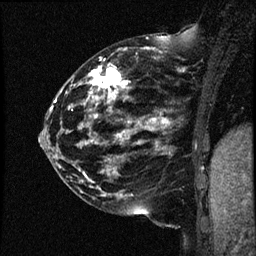
Breast MRI (dynamic contrast-enhanced), one sagittal slice. Slice 19 of 44 in the series (ordered by position). Dynamic contrast-enhanced study with each time point stored as its own series, time point 2 of 4 at this slice position (early post-contrast, ordered by acquisition time). 1.5 T. TE 4.2 ms, TR 17.7 ms. 2 mm slice thickness. 256 × 256 image matrix, field of view 200 × 200 mm. Female patient, age 52 years. From the clinical record (not read from this slice): setting: breast cancer imaged before/during neoadjuvant chemotherapy; receptor status: HR-positive, HER2-negative.
Annotated regions visible in this slice (semi-automatic segmentation, software-assisted and operator-edited):
- analysis volume of interest (the breast-tissue region the enhancement analysis was run in; not a lesion): bounding box (x1, y1, x2, y2) in pixels: (47, 48, 163, 147)
- tumour enhancement mask (voxels above the 100 % enhancement threshold inside the analysis volume of interest): (80, 48, 163, 144)